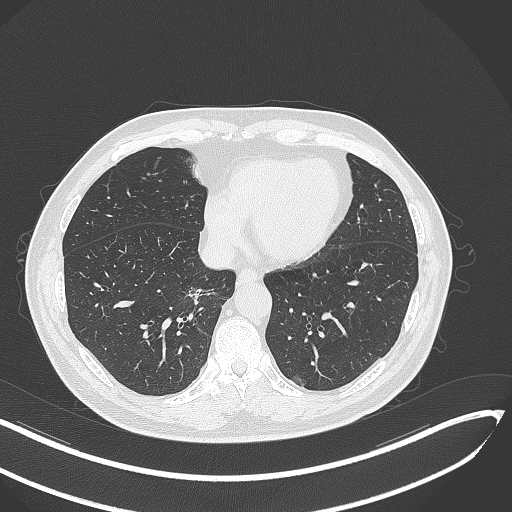
Chest CT, one axial slice. Position 120 of 429 along the scan axis. Reconstruction kernel B70f. 120 kVp. Lung window (W 1500 / L -600 HU). 1 mm slice thickness. 512 × 512 image matrix, field of view 400 × 400 mm. Male patient, age 62 years. From the clinical record (not read from this slice): clinical TNM (as recorded): T1b N0 M0.
Annotated regions visible in this slice (rectangle marked by the reading radiologist):
- lung tumour (recorded histology: adenocarcinoma): bounding box (x1, y1, x2, y2) in pixels: (183, 286, 218, 311)